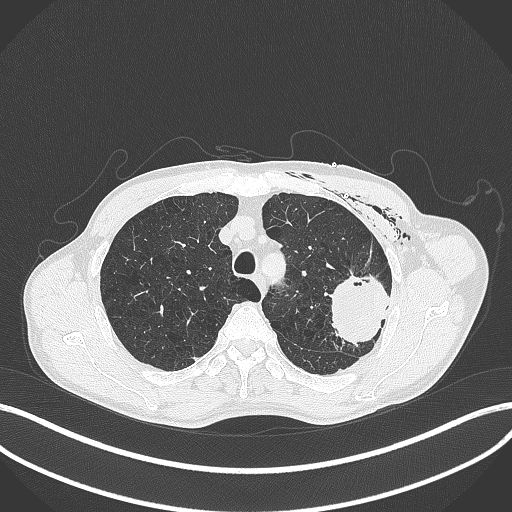
Chest CT, one axial slice; slice 317 of 457 in the series (ordered by position); lung window (W 1500 / L -600 HU); 1 mm slice thickness; 512 × 512 image matrix, field of view 400 × 400 mm. Male patient, age 58 years. Case-level facts recorded for this patient, not image findings: clinical TNM (as recorded): T3 N0 M0.
Annotated regions visible in this slice (rectangle marked by the reading radiologist):
- lung tumour (recorded histology: adenocarcinoma): bounding box [x1, y1, x2, y2] px = [323, 269, 392, 347]